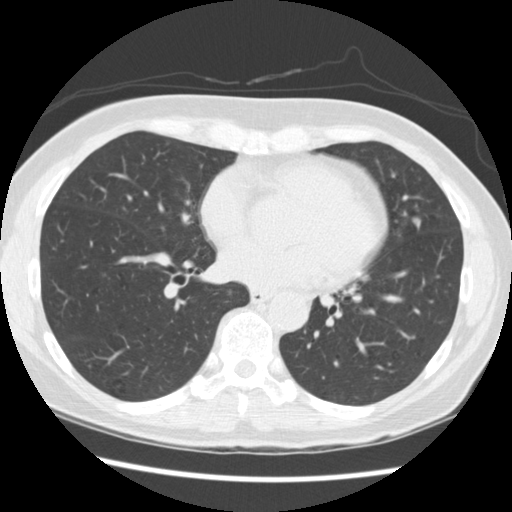
Low-dose screening chest CT, one axial slice; position 120 of 262 along the scan axis; reconstruction kernel STANDARD; 120 kVp; lung window (W 1500 / L -600 HU); 2.5 mm slice thickness; 512 × 512 image matrix, field of view 340 × 340 mm.
Structures marked on this image (outlined manually by an expert reader):
- lesion 2 (tumor, lingular bronchus): bounding box <412,217,421,226> (left, top, right, bottom; pixels)